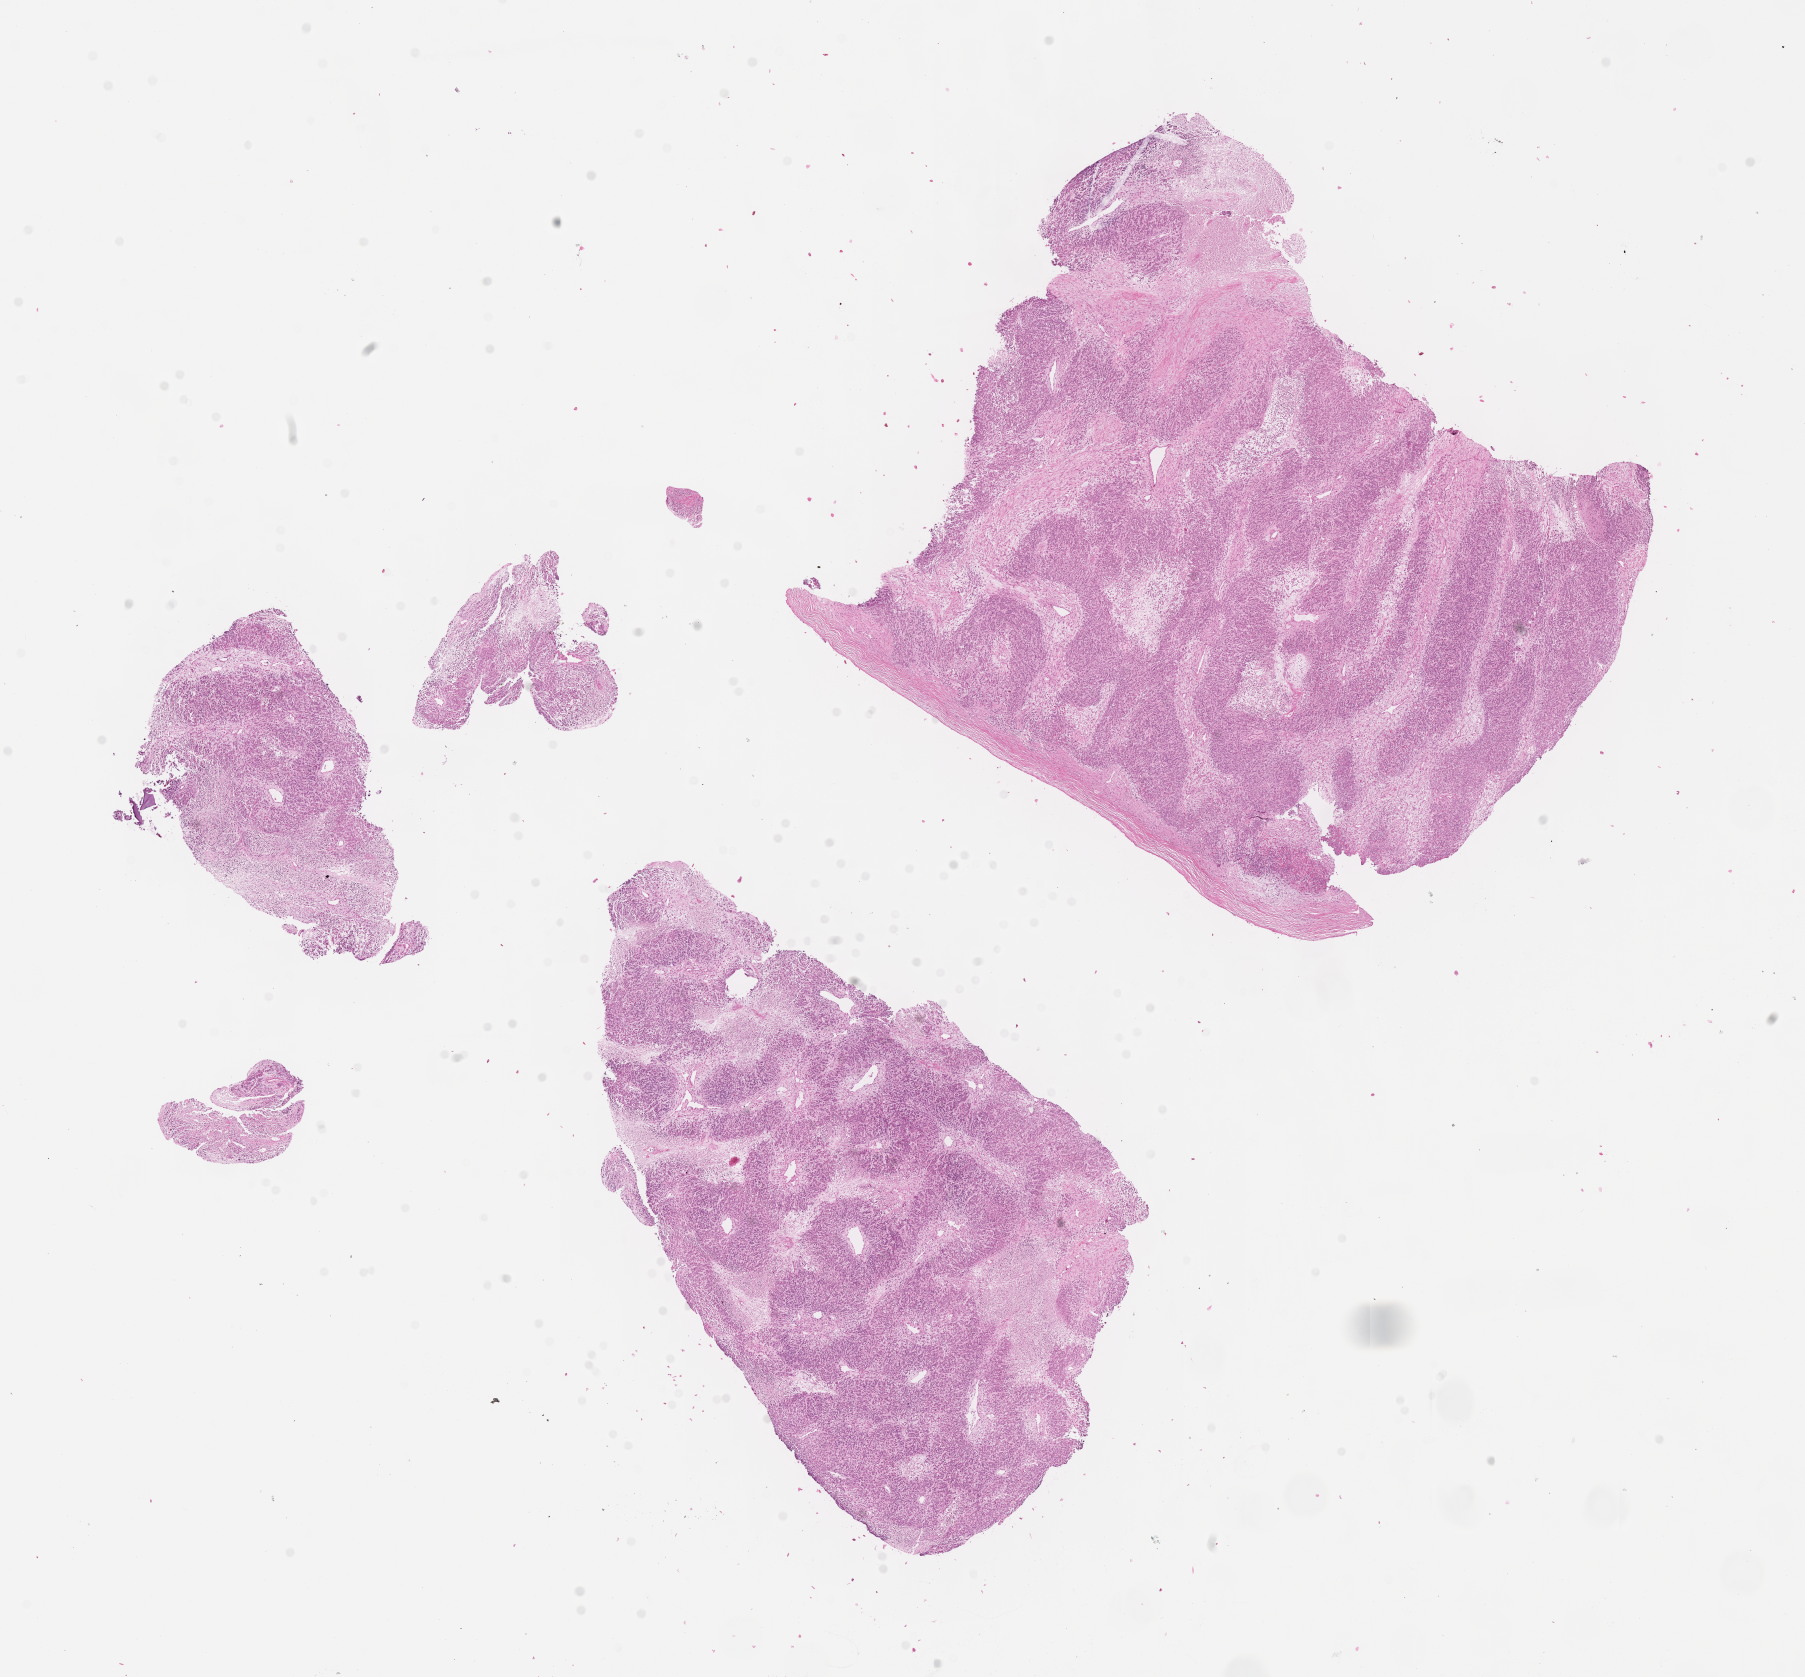
Whole-slide image, H&E stain of tumor tissue, whole scanned area (about 14.6 x 13.6 mm) shown as a low-resolution overview, FFPE section, sample anatomic site: abdomen/pelvis. Patient: female, age 3.8 years at diagnosis.
Diagnosis: rhabdomyosarcoma; histological classification: embryonal rhabdomyosarcoma. Primary site (case record): retroperitoneum. Stage (as recorded): 4. Metastatic status at presentation (as recorded): metastatic (confirmed).